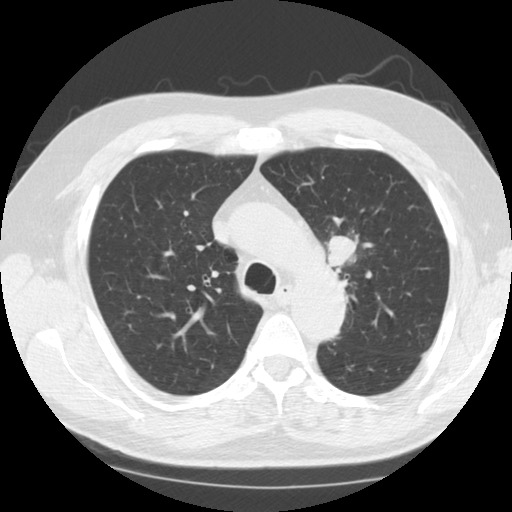
Axial slice from a low-dose chest CT screening exam; third screening round (two years after baseline); lung window (W 1500 / L -600 HU); 2.5 mm slice thickness; standard (soft-tissue) reconstruction kernel (STANDARD); slice 34 of 124 in the series. Male, age 60 years at enrolment. Current smoker at enrolment.
• Expert-annotated lung lesion, bounding box [x1, y1, x2, y2] px = [317, 225, 370, 282].
• Screening reader's record for this exam (one nodule recorded; not confirmed to be the boxed lesion): non-calcified nodule or mass ≥4 mm, left upper lobe, 24 × 21 mm, smooth margins, soft tissue attenuation, pre-existing on the prior screen: no.
• Lung cancer was diagnosed 14 days after this screen: small cell carcinoma, NOS, left upper lobe, stage IIA (AJCC 6th edition), 26 mm at pathology.